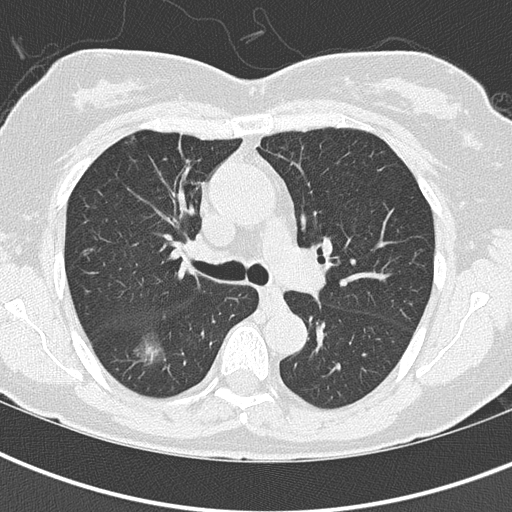
Chest CT (low-dose screening protocol), one axial image. Baseline screening round. Lung window (W 1500 / L -600 HU). Lung (sharp) reconstruction kernel (B50f). Slice 63 of 200 in the series. Female participant, aged 68 years at enrolment. Former smoker at enrolment.
• Expert reader's lesion annotation, bounding box (x1, y1, x2, y2) in pixels: (119, 326, 178, 377).
• The exam's reader record, not a measurement of the box and not confirmed to be the same lesion: non-calcified nodule or mass ≥4 mm, right lower lobe, 19 × 17 mm, spiculated (stellate) margins, ground glass attenuation.
• Official screen result: positive, change unspecified: nodule(s) >= 4 mm or enlarging nodule(s), mass(es), or other non-specific abnormalities suspicious for lung cancer.
• Participant outcome: lung cancer diagnosed 40 days after this screen — bronchiolo-alveolar adenocarcinoma, NOS, right lower lobe, well differentiated (G1), stage IA (AJCC 6th edition), 15 mm at pathology.